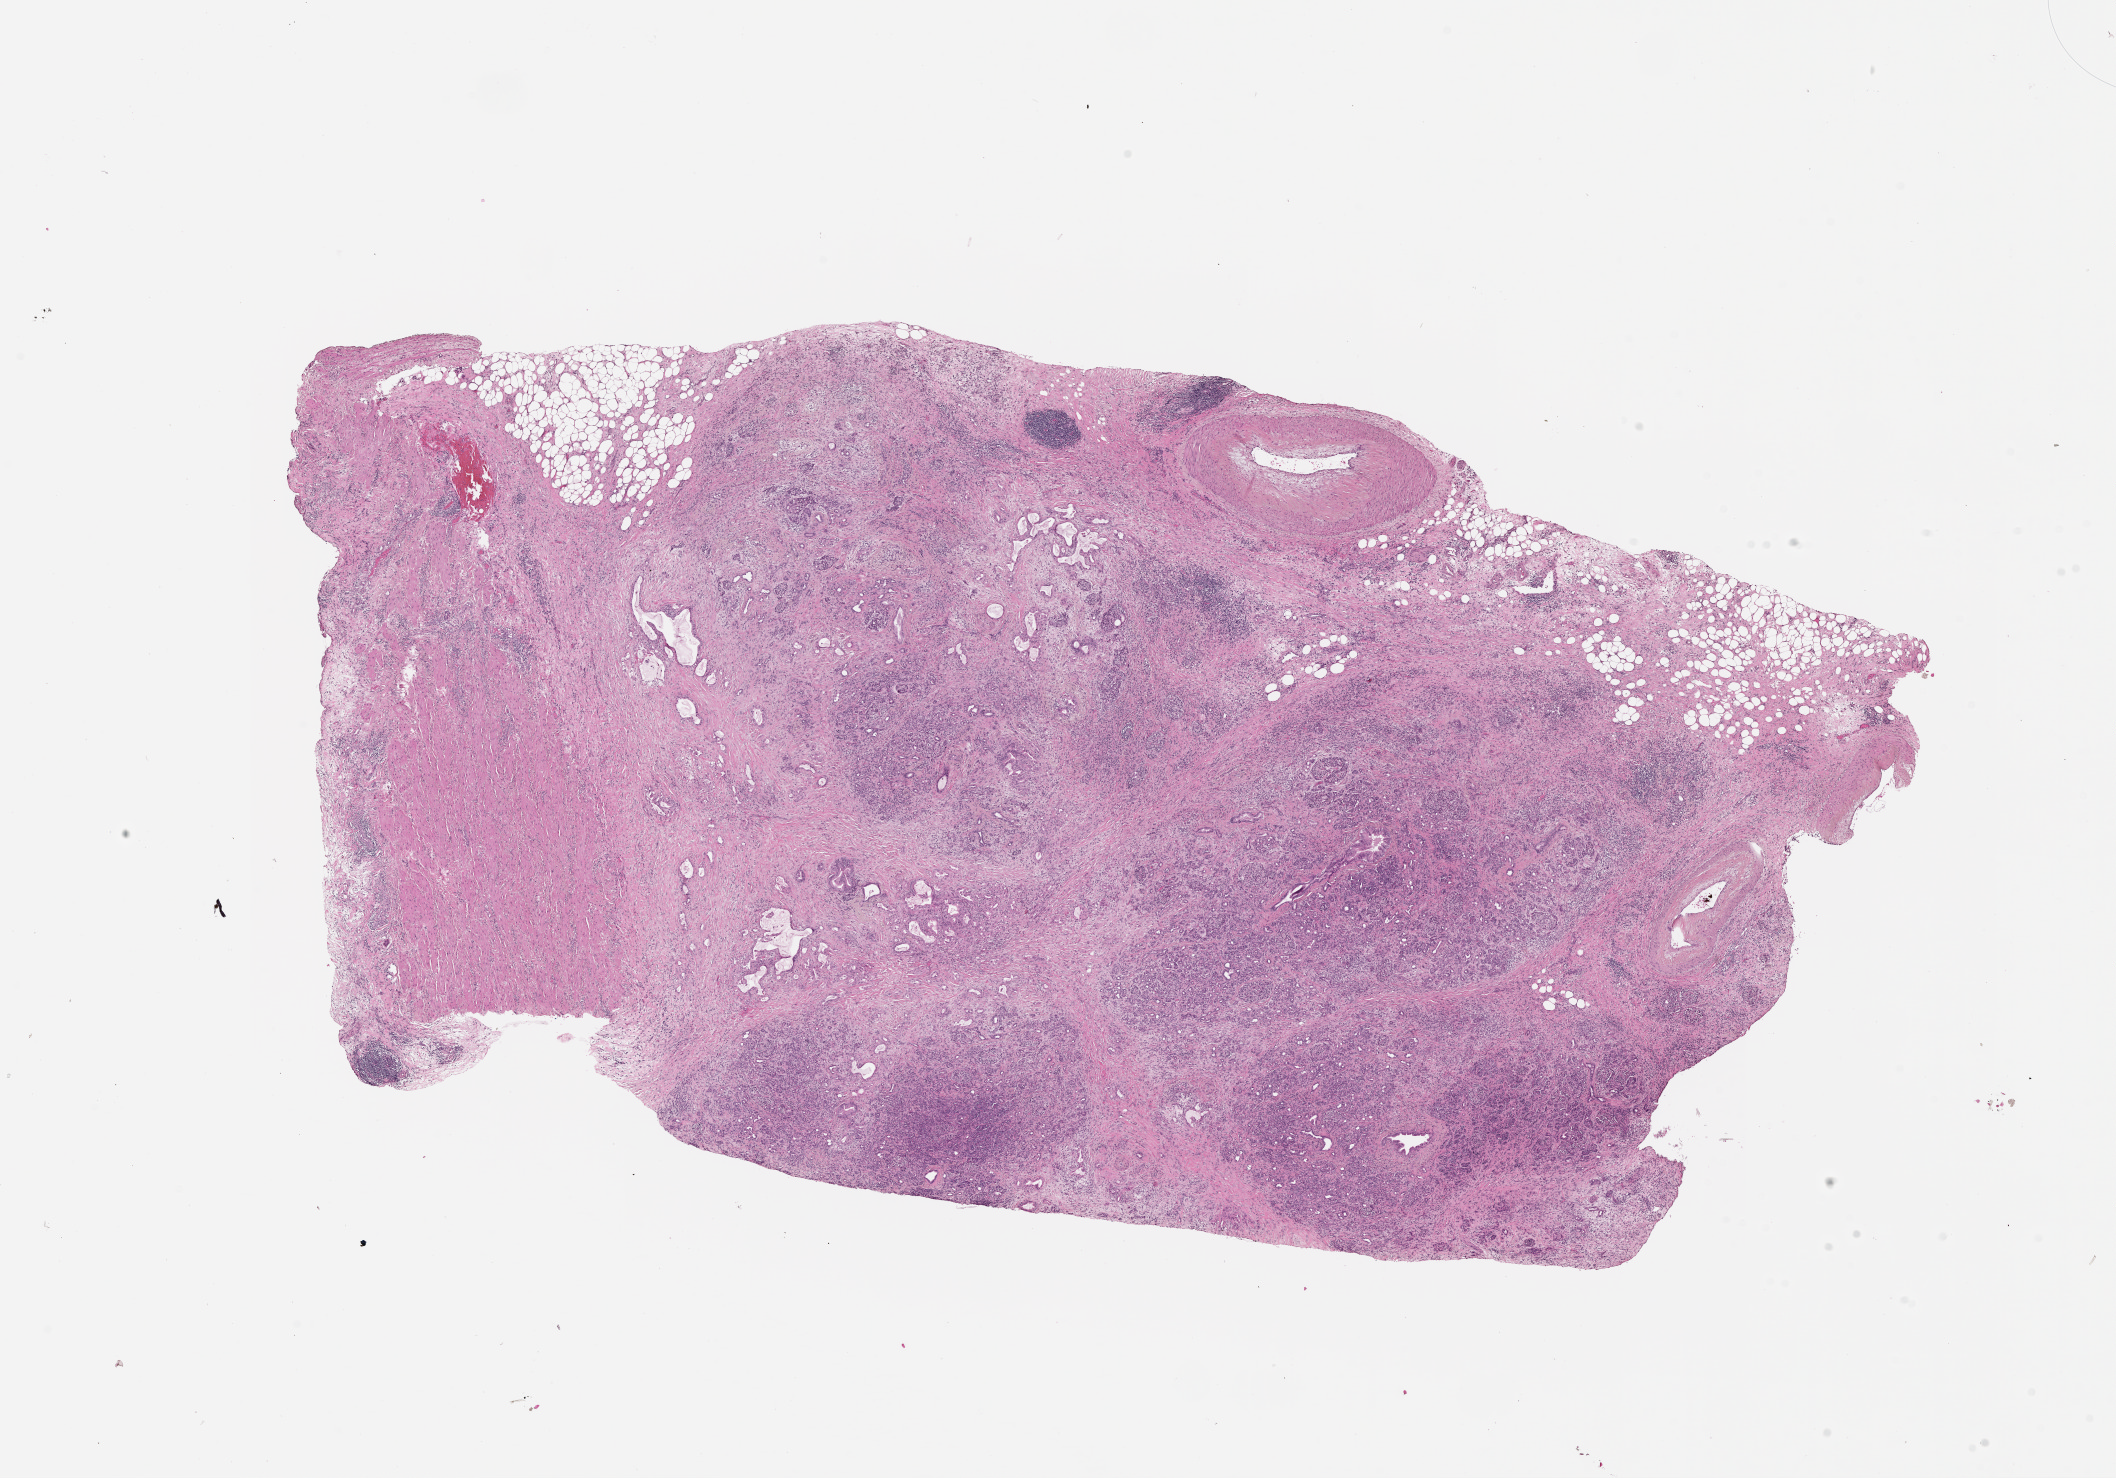
Hematoxylin and eosin (H&E) stained whole-slide image — a low-resolution overview of the entire scanned area, about 17.0 x 11.9 mm (acquisition: 20x scan); tumour tissue sample, sampled site: pancreas. Male, 78 y/o. Histologic grade: G2 (moderately differentiated). Pathologist review of this section (percent, as recorded): tumour nuclei 10%, necrosis 0%.
• primary tumour site (as recorded): tail
• AJCC pathologic stage: III
• diagnosis: Infiltrating duct carcinoma, NOS